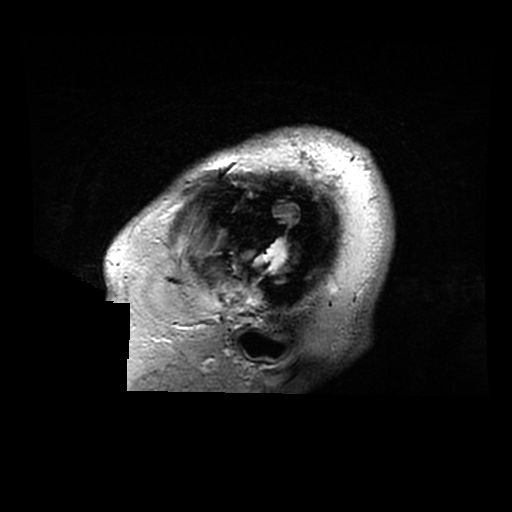
Brain MRI from a brain-tumour surgery series, one sagittal slice; 0.6 mm slice thickness; 512 × 512 image matrix, field of view 240 × 240 mm. From the clinical record (not read from this slice): histopathology: Astrocytoma; WHO grade: 2; IDH mutation: yes.
Annotated regions visible in this slice (outlined manually by an expert reader):
- tumour: box from (x=257, y=238) to (x=293, y=269) px